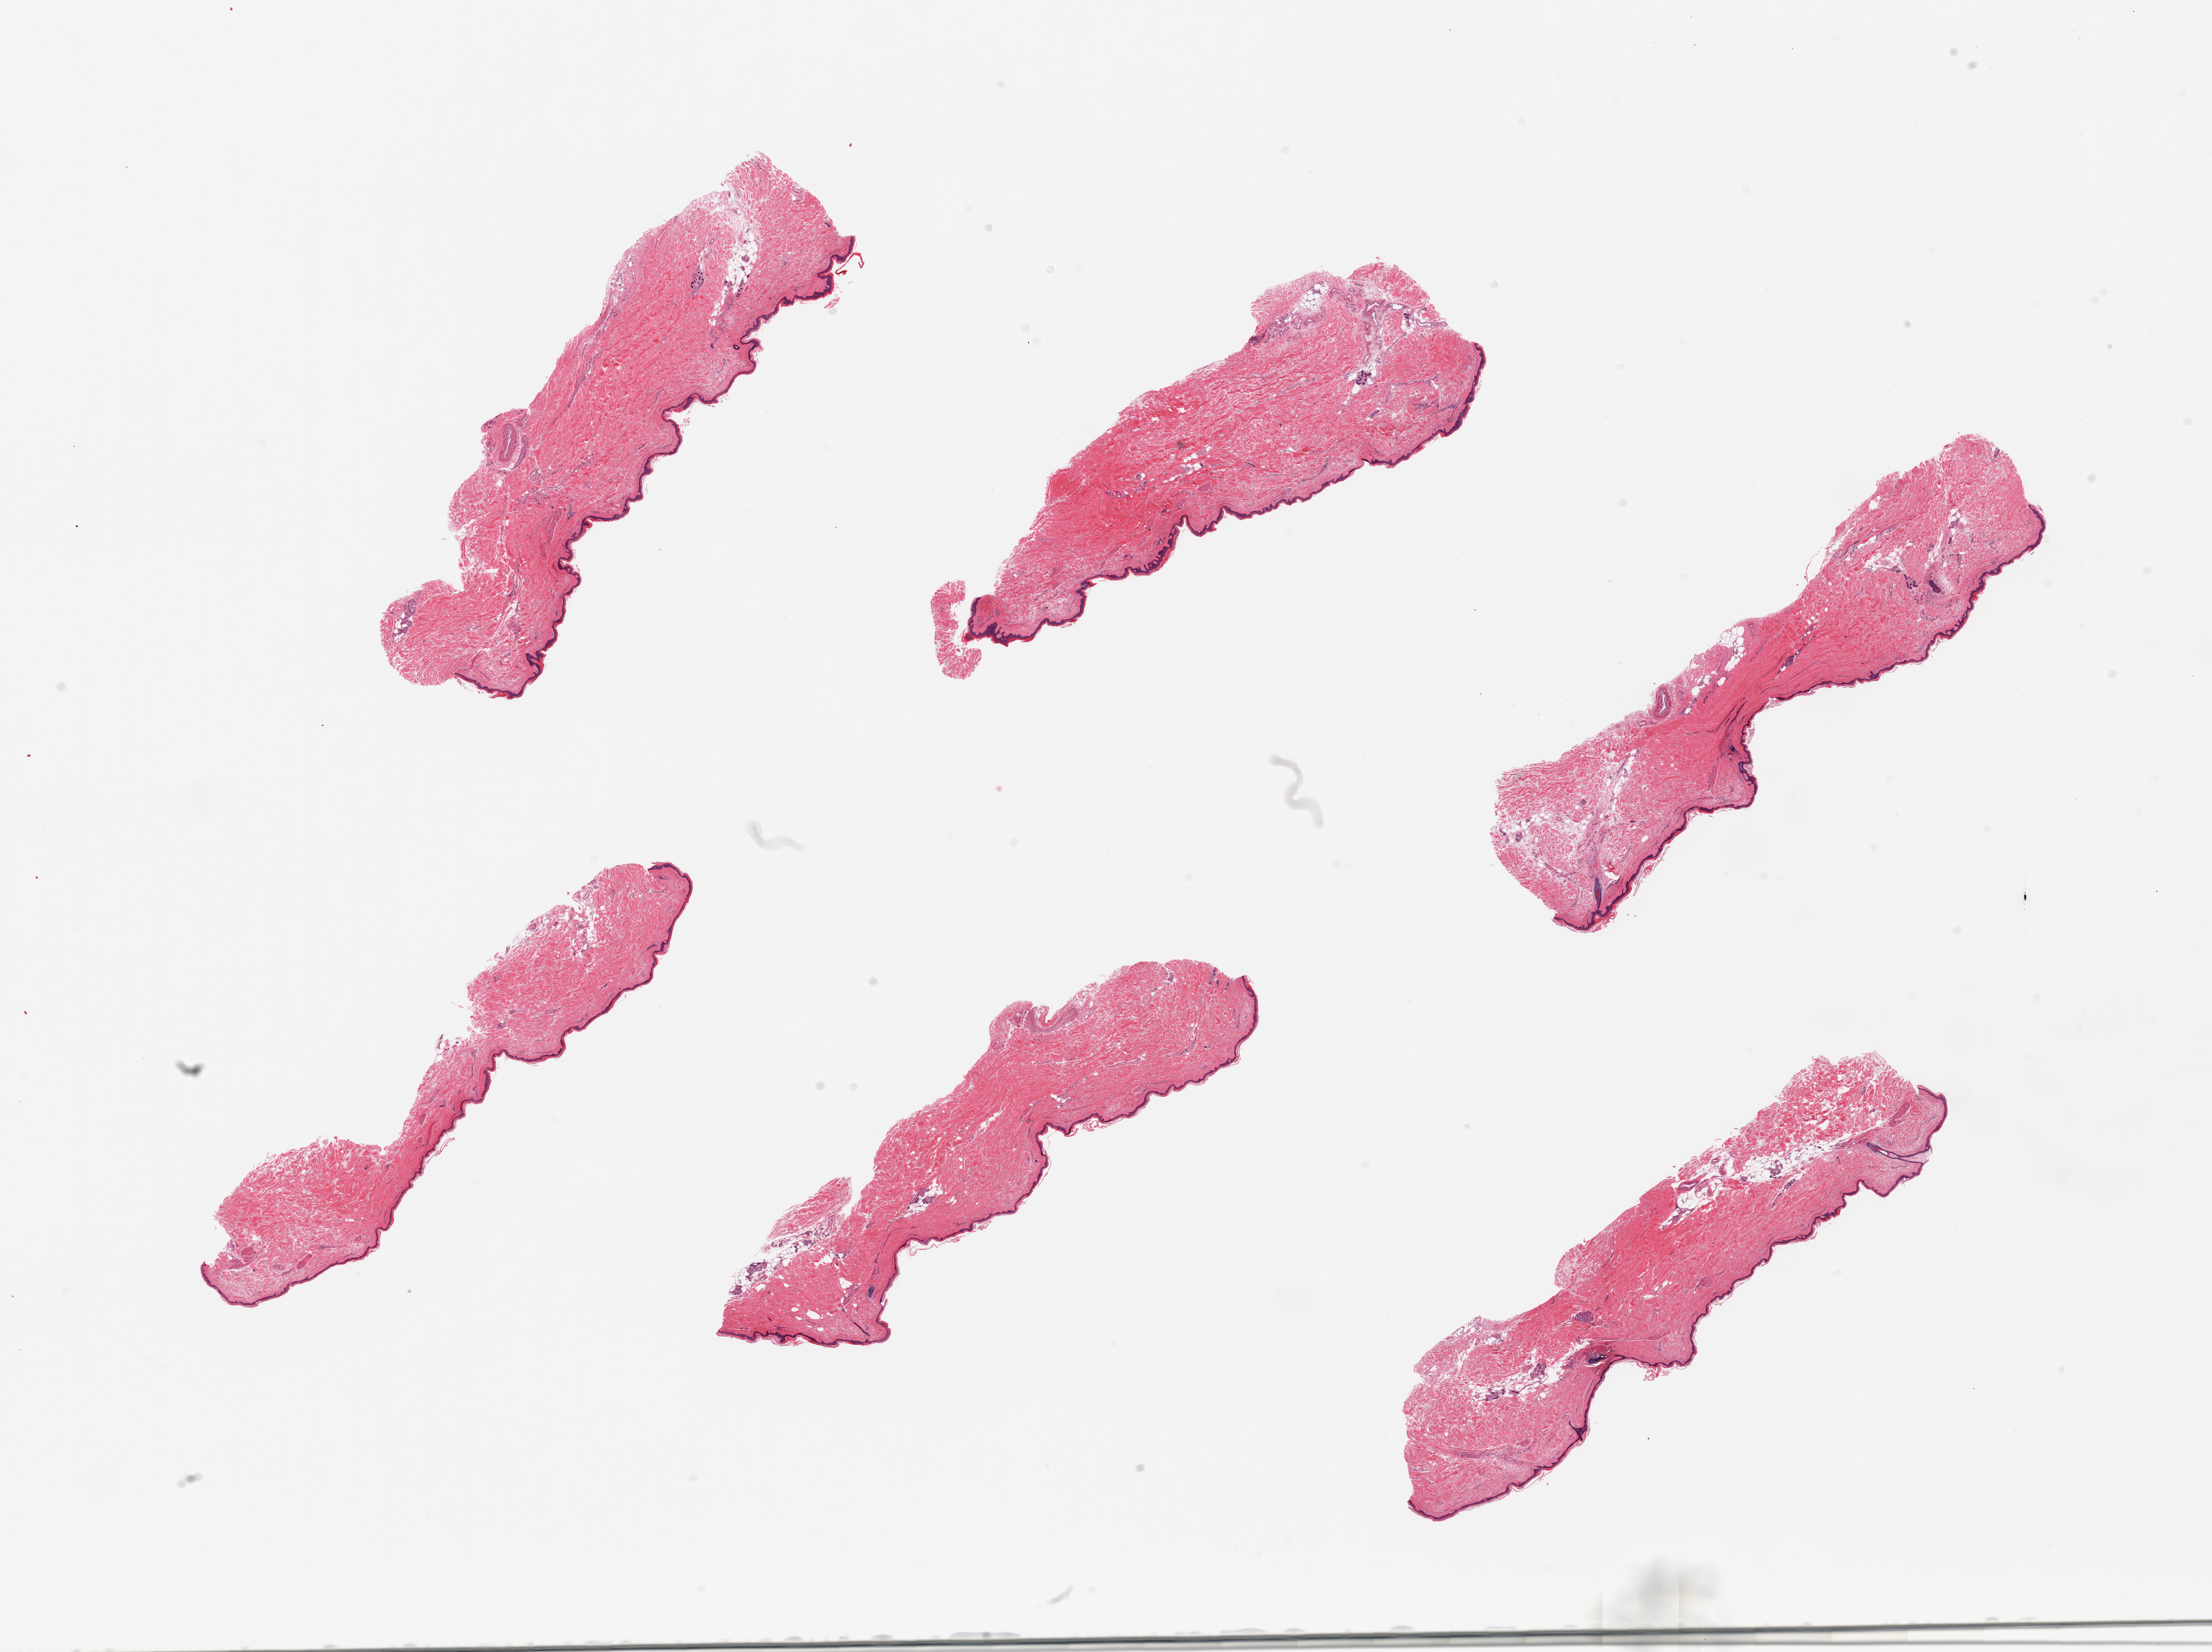
Whole-slide image, haematoxylin and eosin stain, brightfield — shown as a low-resolution overview of the whole scanned area (about 28.5 x 21.3 mm, slide scanned at 20x); PAXgene-fixed paraffin-embedded (PFPE) section; target tissue: skin of lower leg; tissue donor sample. Male donor.
Pathologist's review note for this sample: 6 pieces; well trimmed, epidermis measures 30 microns.